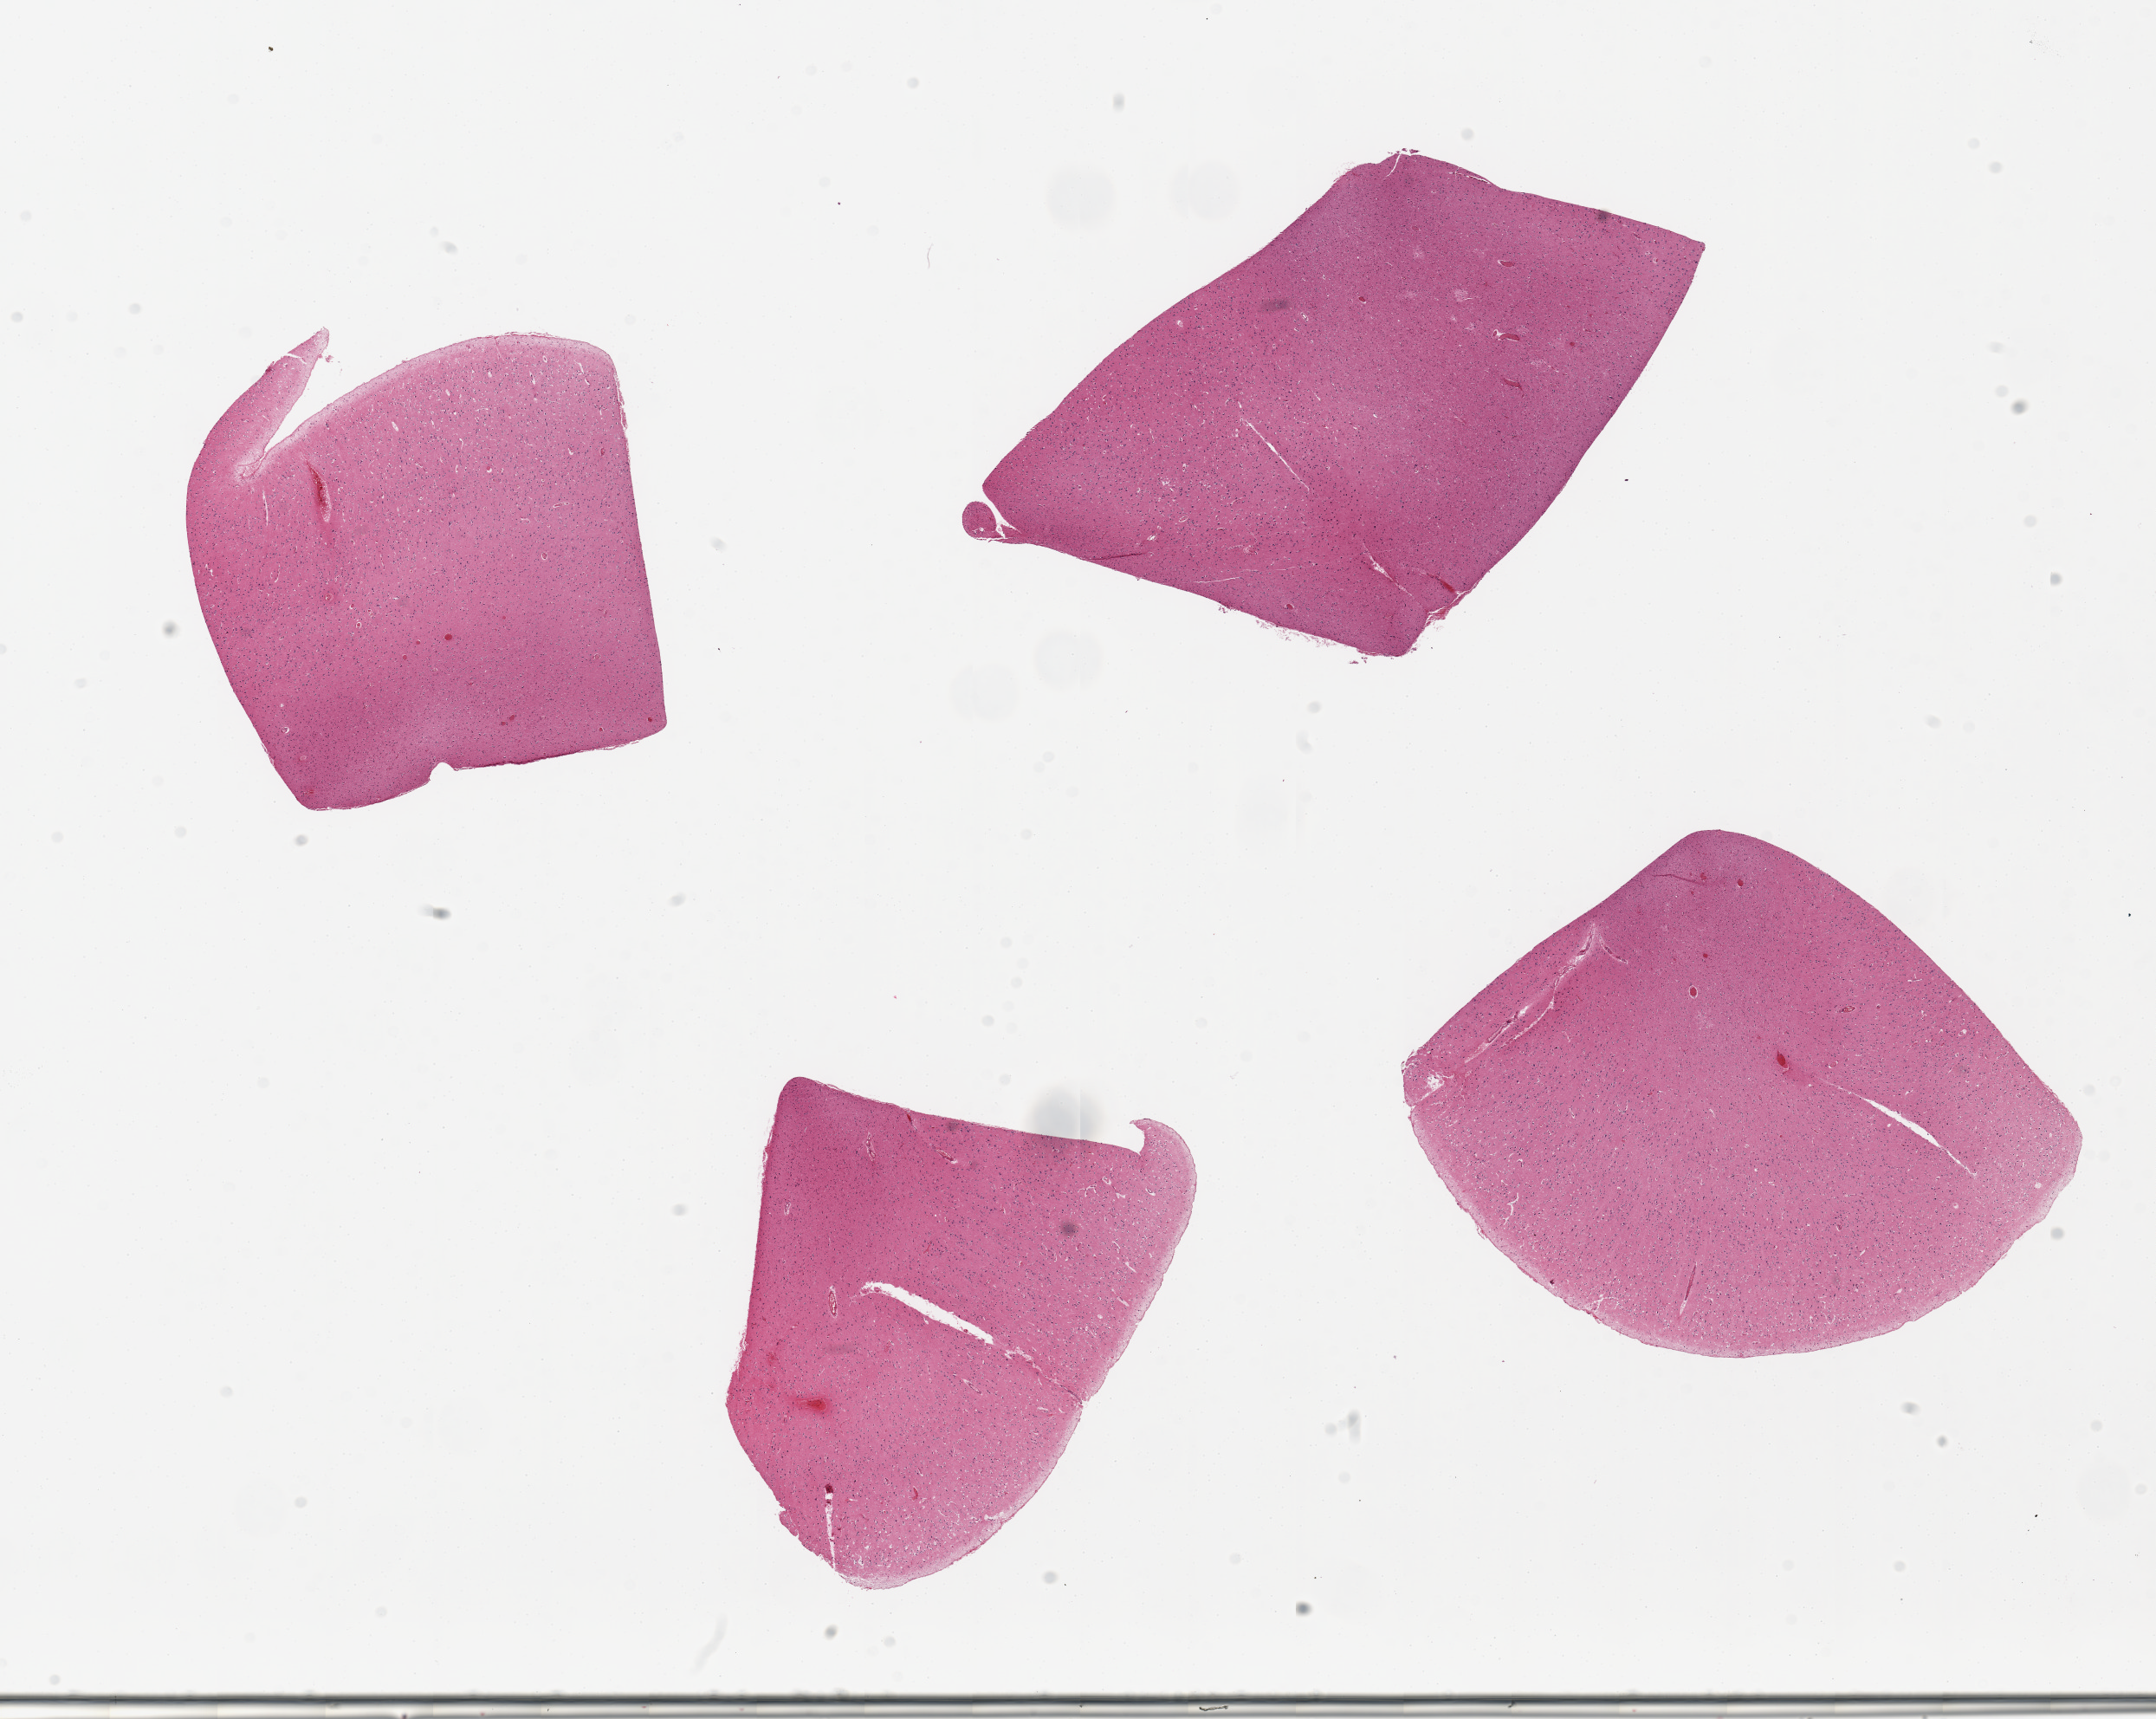
Digitized H&E-stained section — a low-resolution overview of the entire scanned area, about 19.7 x 15.7 mm; PAXgene-fixed paraffin-embedded (PFPE) section; target tissue: cerebral cortex; tissue donor sample.
Review note (as recorded): 4 pieces; no hemorrhage.